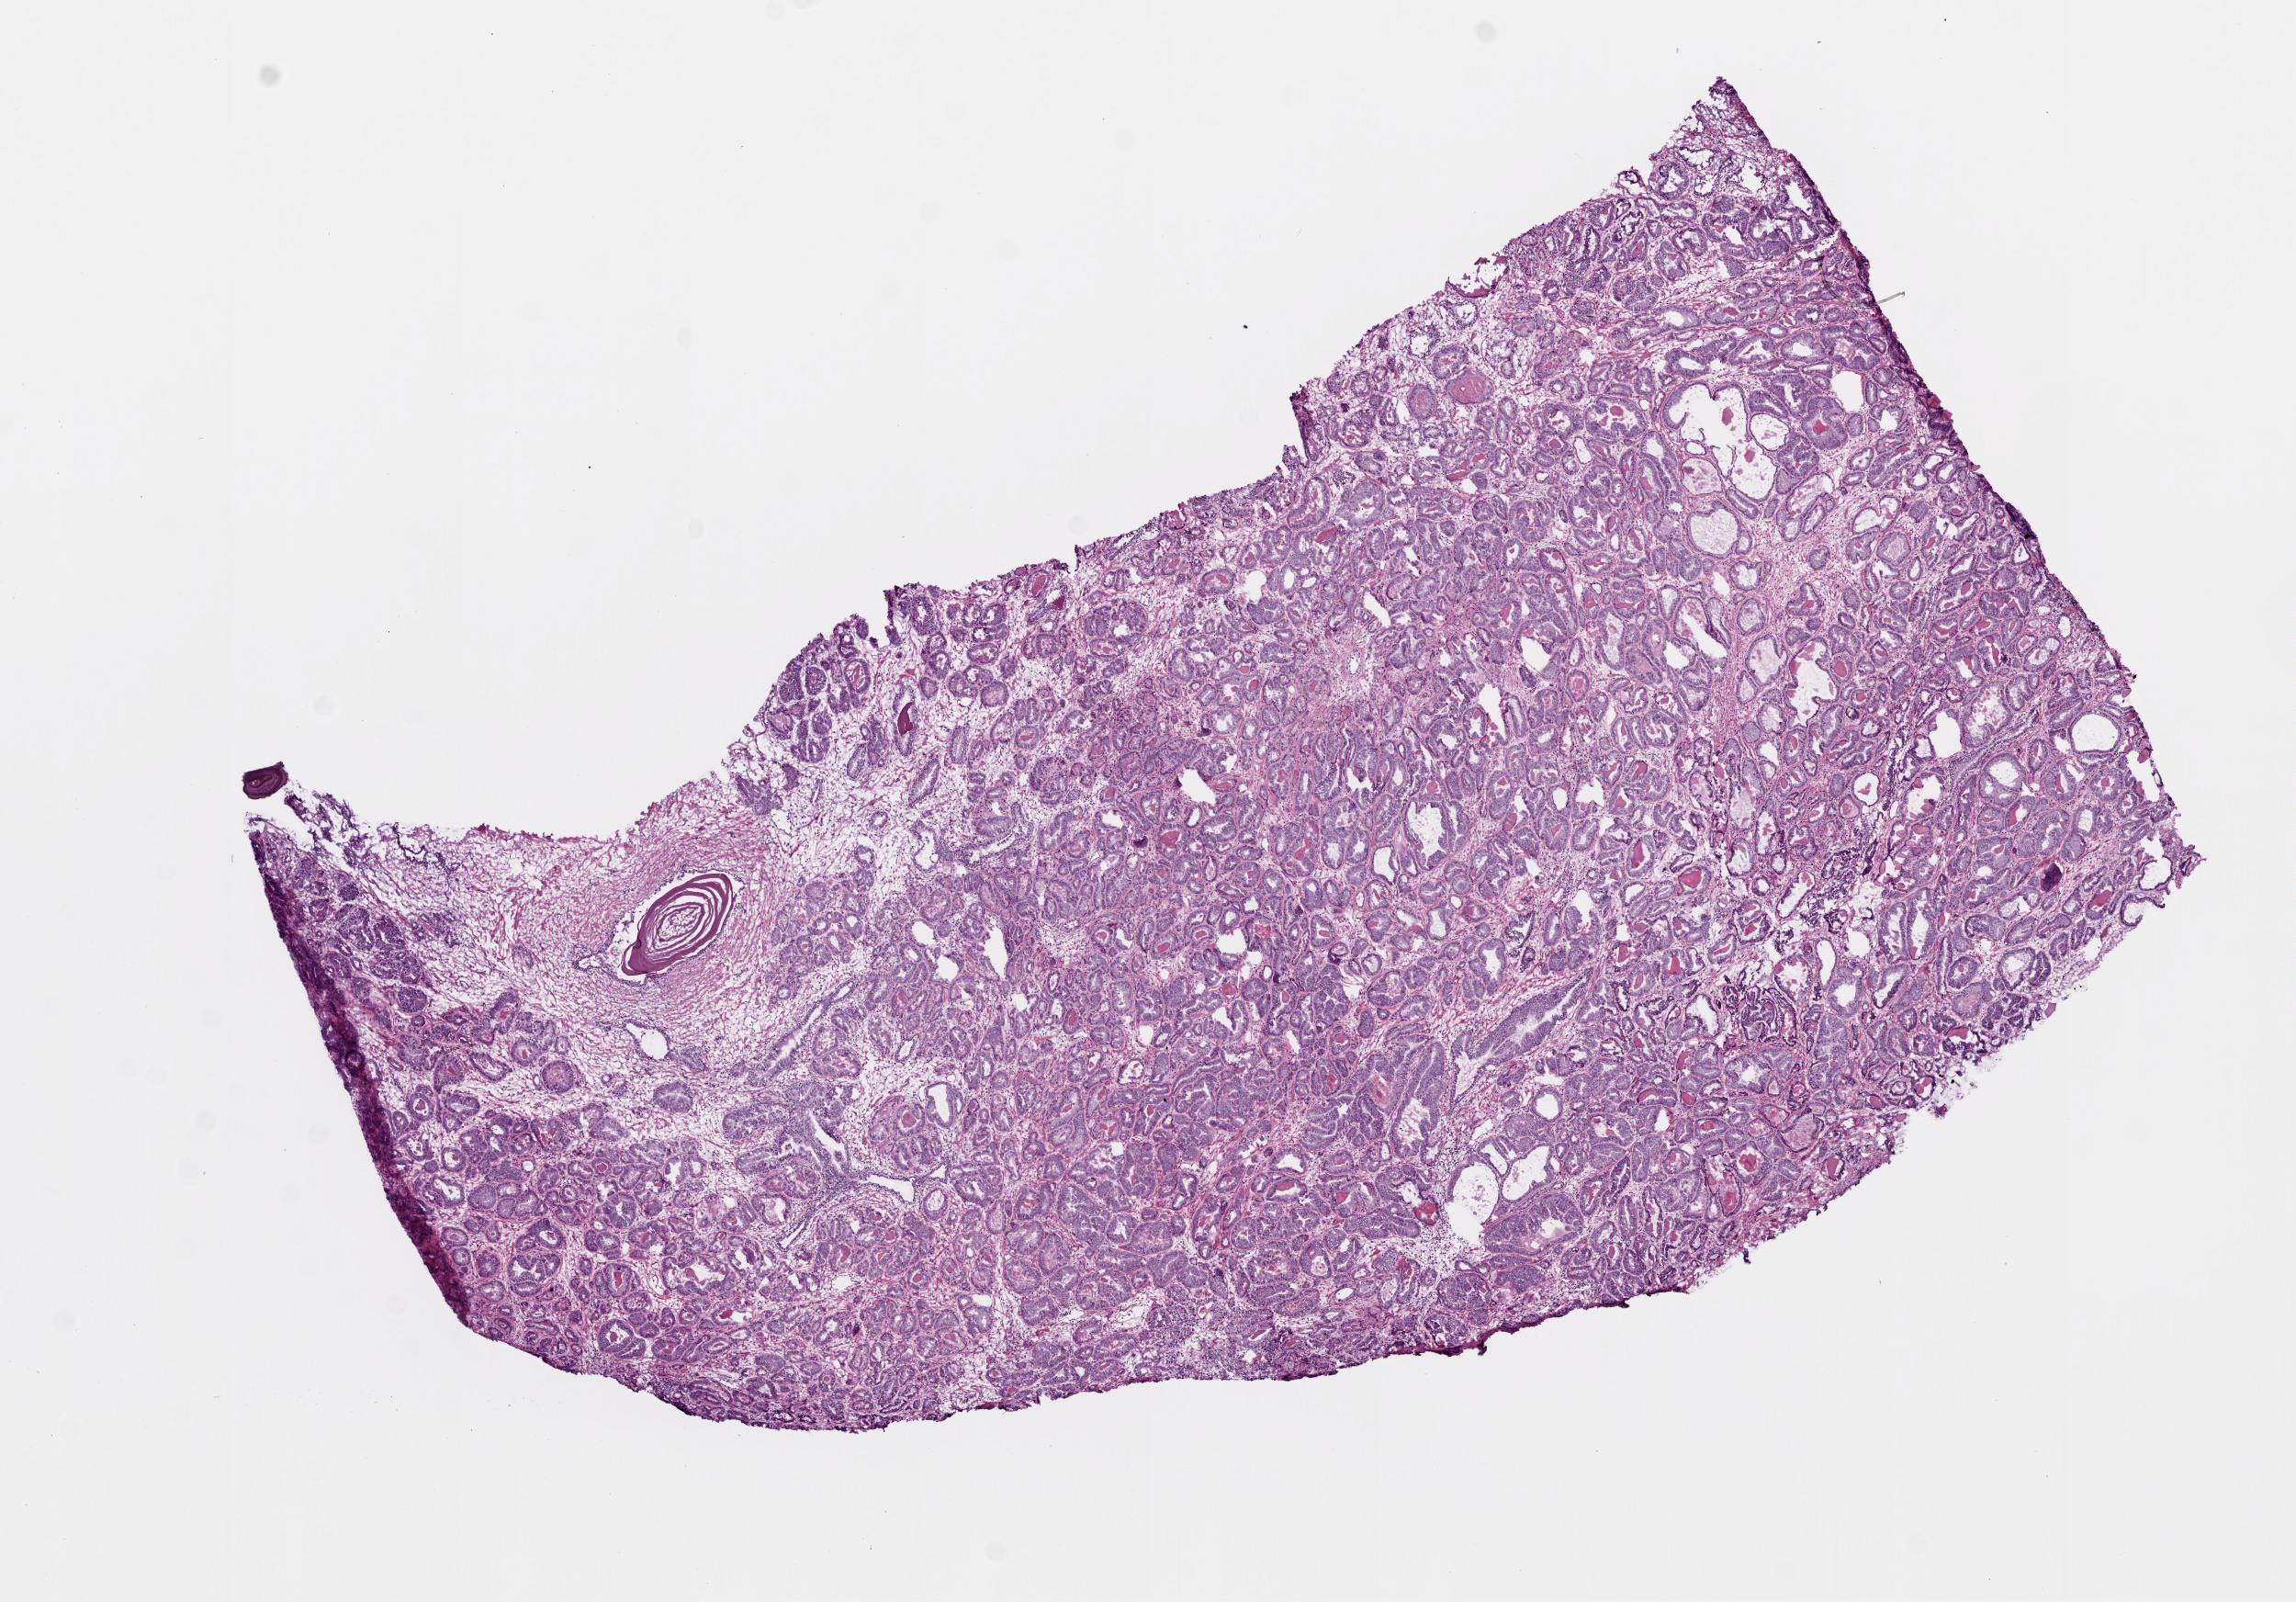
Digitized H&E tissue section (whole slide), a low-resolution overview of the entire scanned area, about 10.0 x 7.0 mm (from a 20x scan). Frozen section. Prostate, primary tumour sample. Patient: male, age at initial diagnosis 72 years. Gleason score: 7 (3+4). Slide review estimates, as recorded: tumour cells 75%, tumour nuclei 80%, normal cells 15%, stromal cells 10%, necrosis 0%. Inflammatory infiltration, as recorded: lymphocyte infiltration 0%, monocyte infiltration 0%, neutrophil infiltration 0%.
• lymph nodes positive (case pathology): 0 of 7 examined
• laterality: bilateral
• pathologic diagnosis: Acinar cell carcinoma (prostate gland)